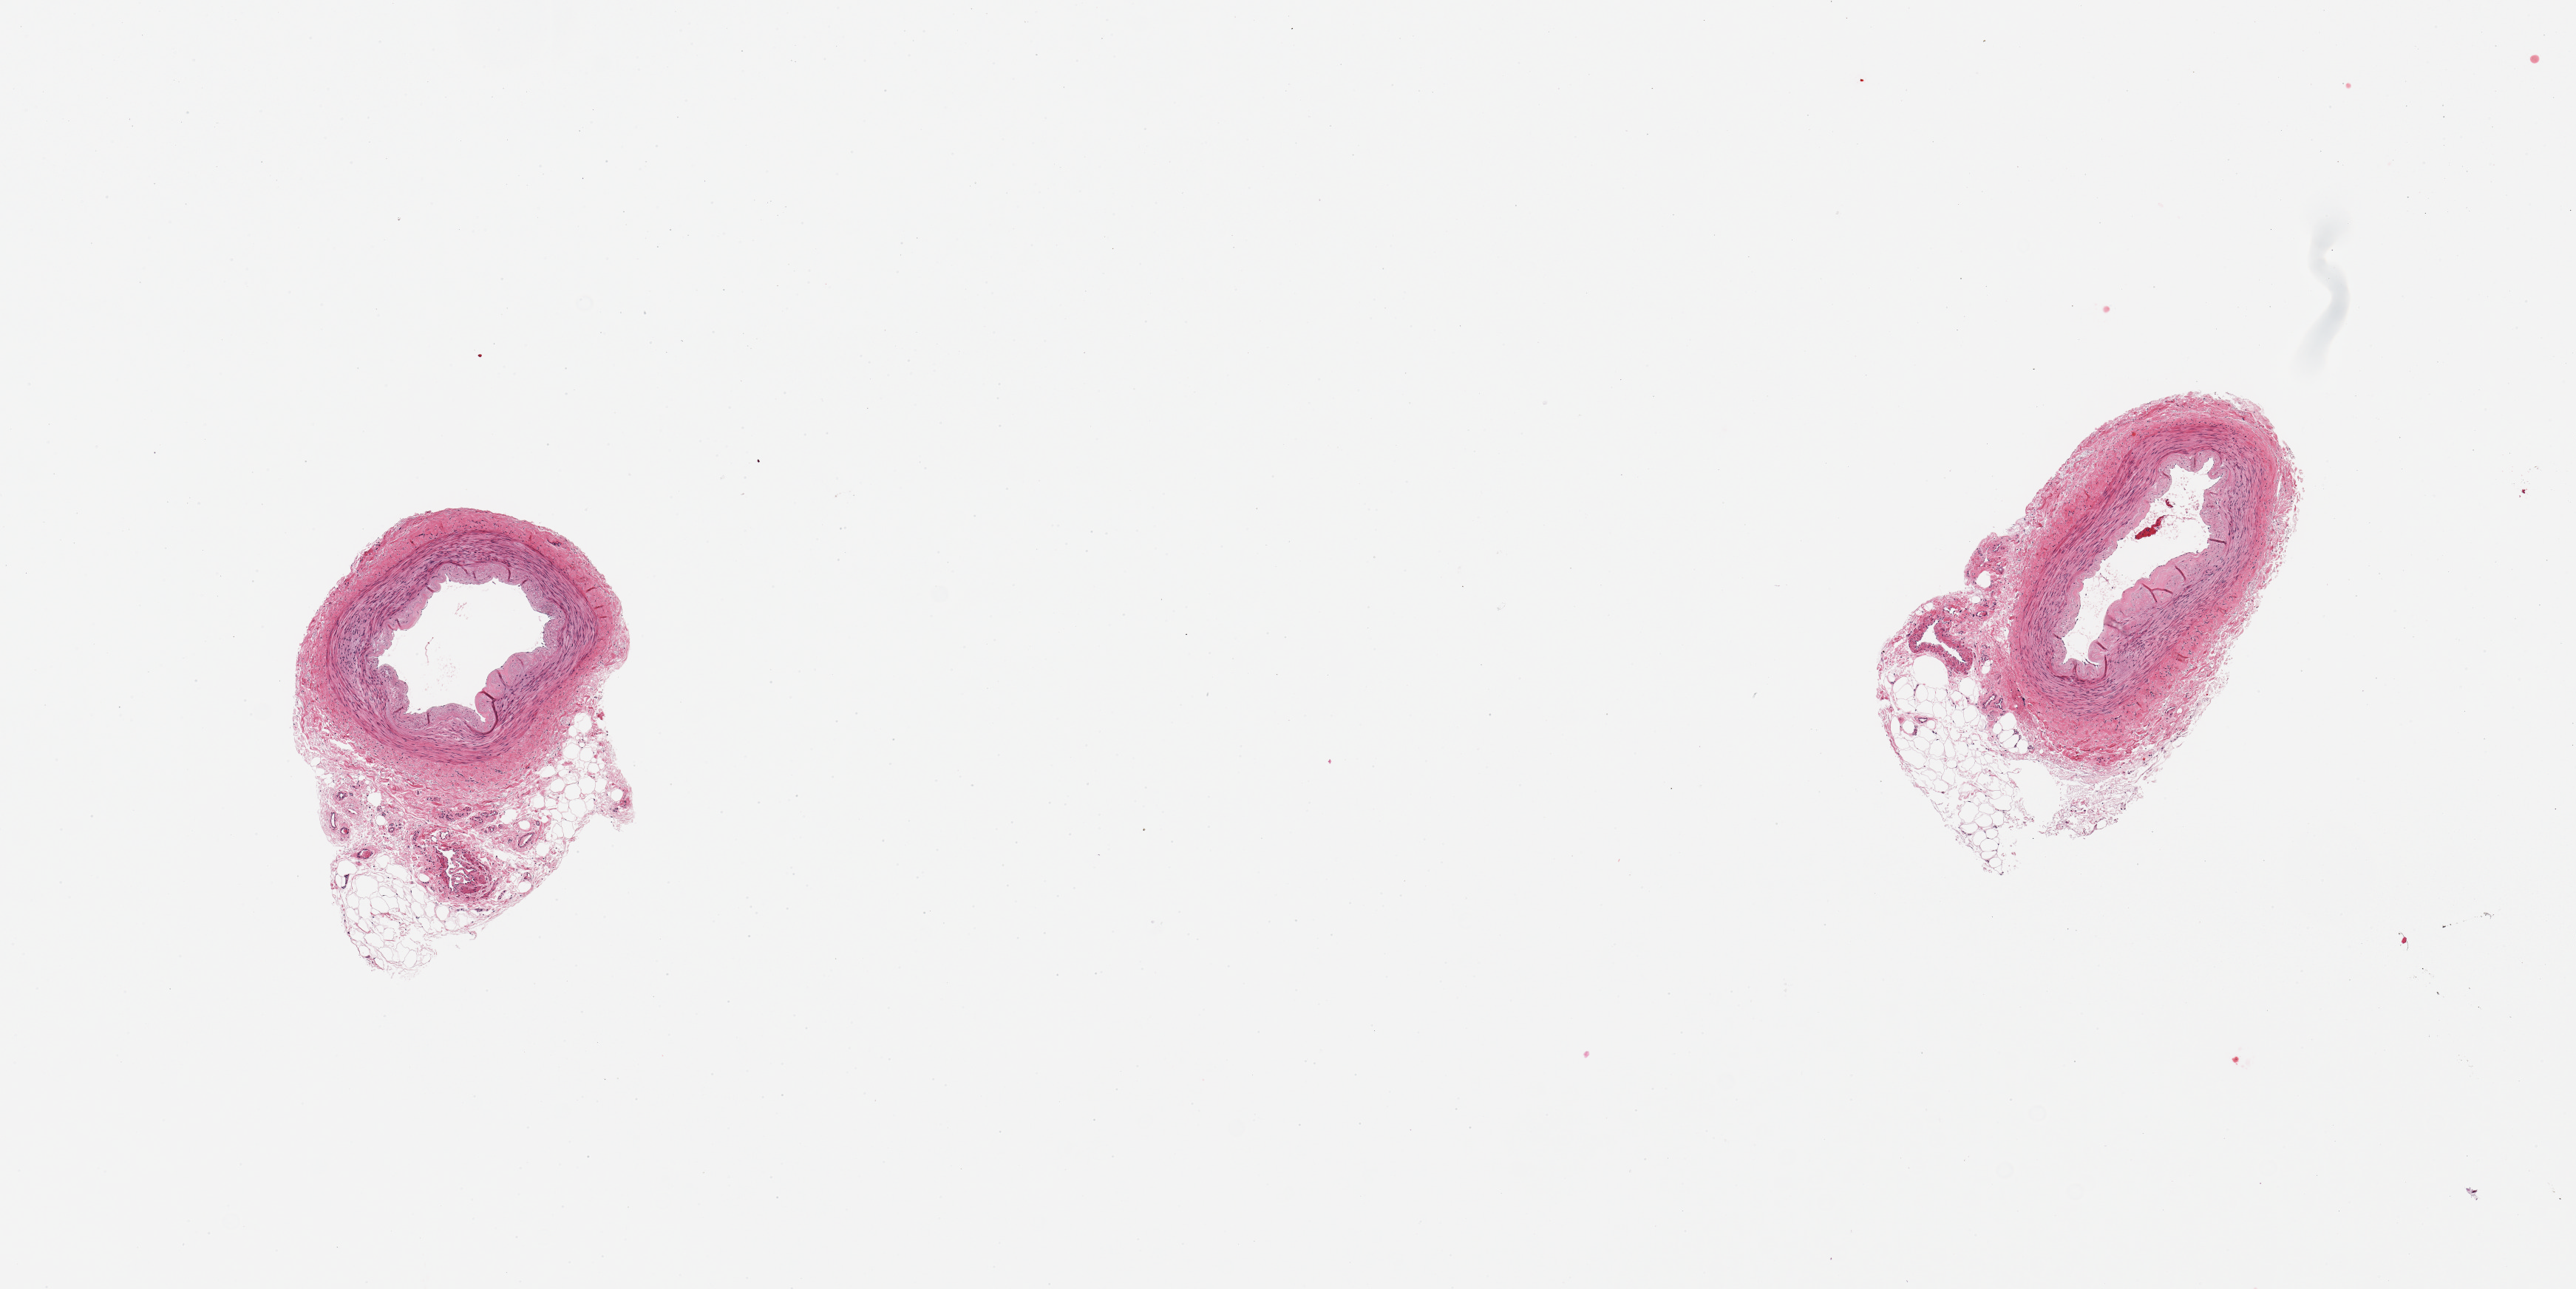
H&E whole-slide image — low-resolution overview of the scanned area, about 13.8 x 6.9 mm. PAXgene-fixed paraffin-embedded (PFPE) section. Target tissue: tibial artery. Tissue donor sample.
• review note (as recorded): 2 pieces; minimal plaque; 25% external fat